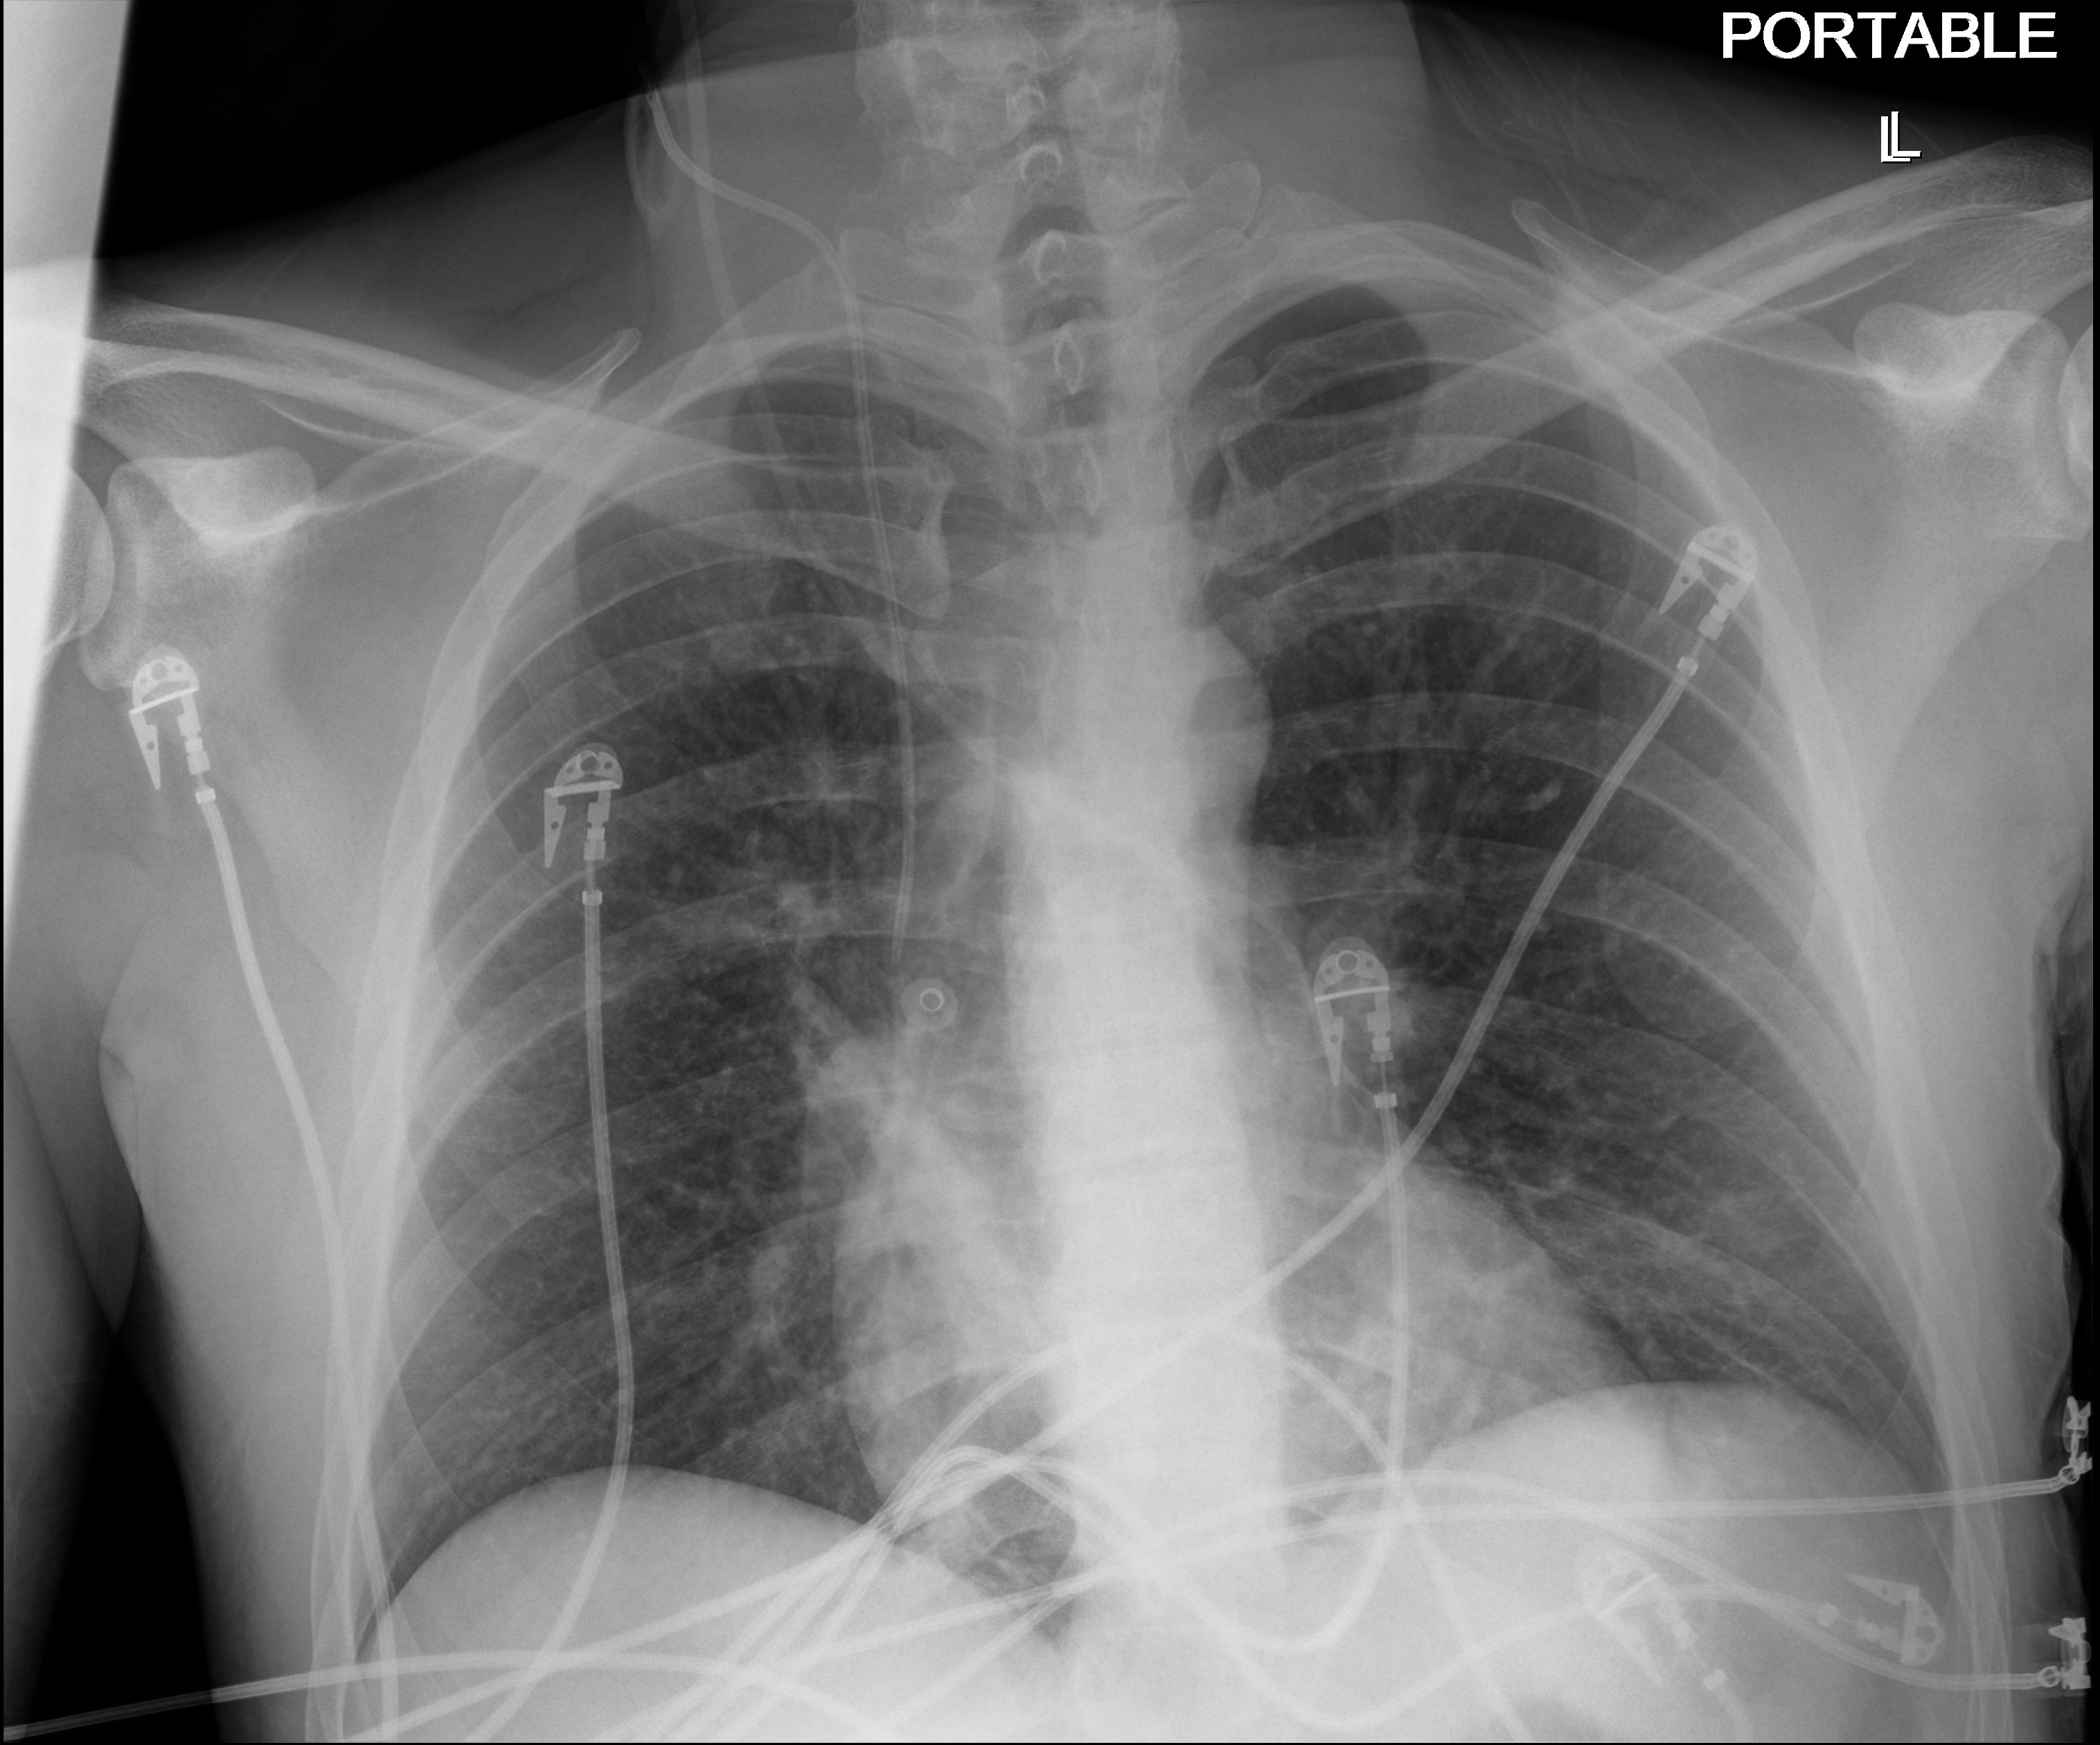
Bedside chest radiograph (digital radiography), anteroposterior (AP) projection. Male patient hospitalised with COVID-19, age 18–59 years.
From the hospital-stay record, not from the radiograph (when in the stay this image was taken is not recorded):
- mechanically ventilated during this hospital stay: yes